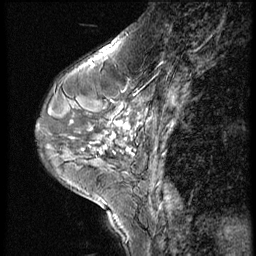
Breast MRI (dynamic contrast-enhanced), one sagittal slice; 3 images stored at this slice position (order not interpretable as contrast timing); 1.5 T; TE 4.2 ms, TR 9 ms; 256 × 256 image matrix, field of view 180 × 180 mm. Patient: female, 46 years. Case-level facts recorded for this patient, not image findings: setting: breast cancer imaged before/during neoadjuvant chemotherapy; receptor status: HER2-positive.
Annotated regions visible in this slice (semi-automatic segmentation, software-assisted and operator-edited):
- analysis volume of interest (the breast-tissue region the enhancement analysis was run in; not a lesion): bounding box (x1, y1, x2, y2) in pixels: (73, 86, 164, 161)
- tumour enhancement mask (voxels above the 140 % enhancement threshold inside the analysis volume of interest): (106, 121, 131, 150)